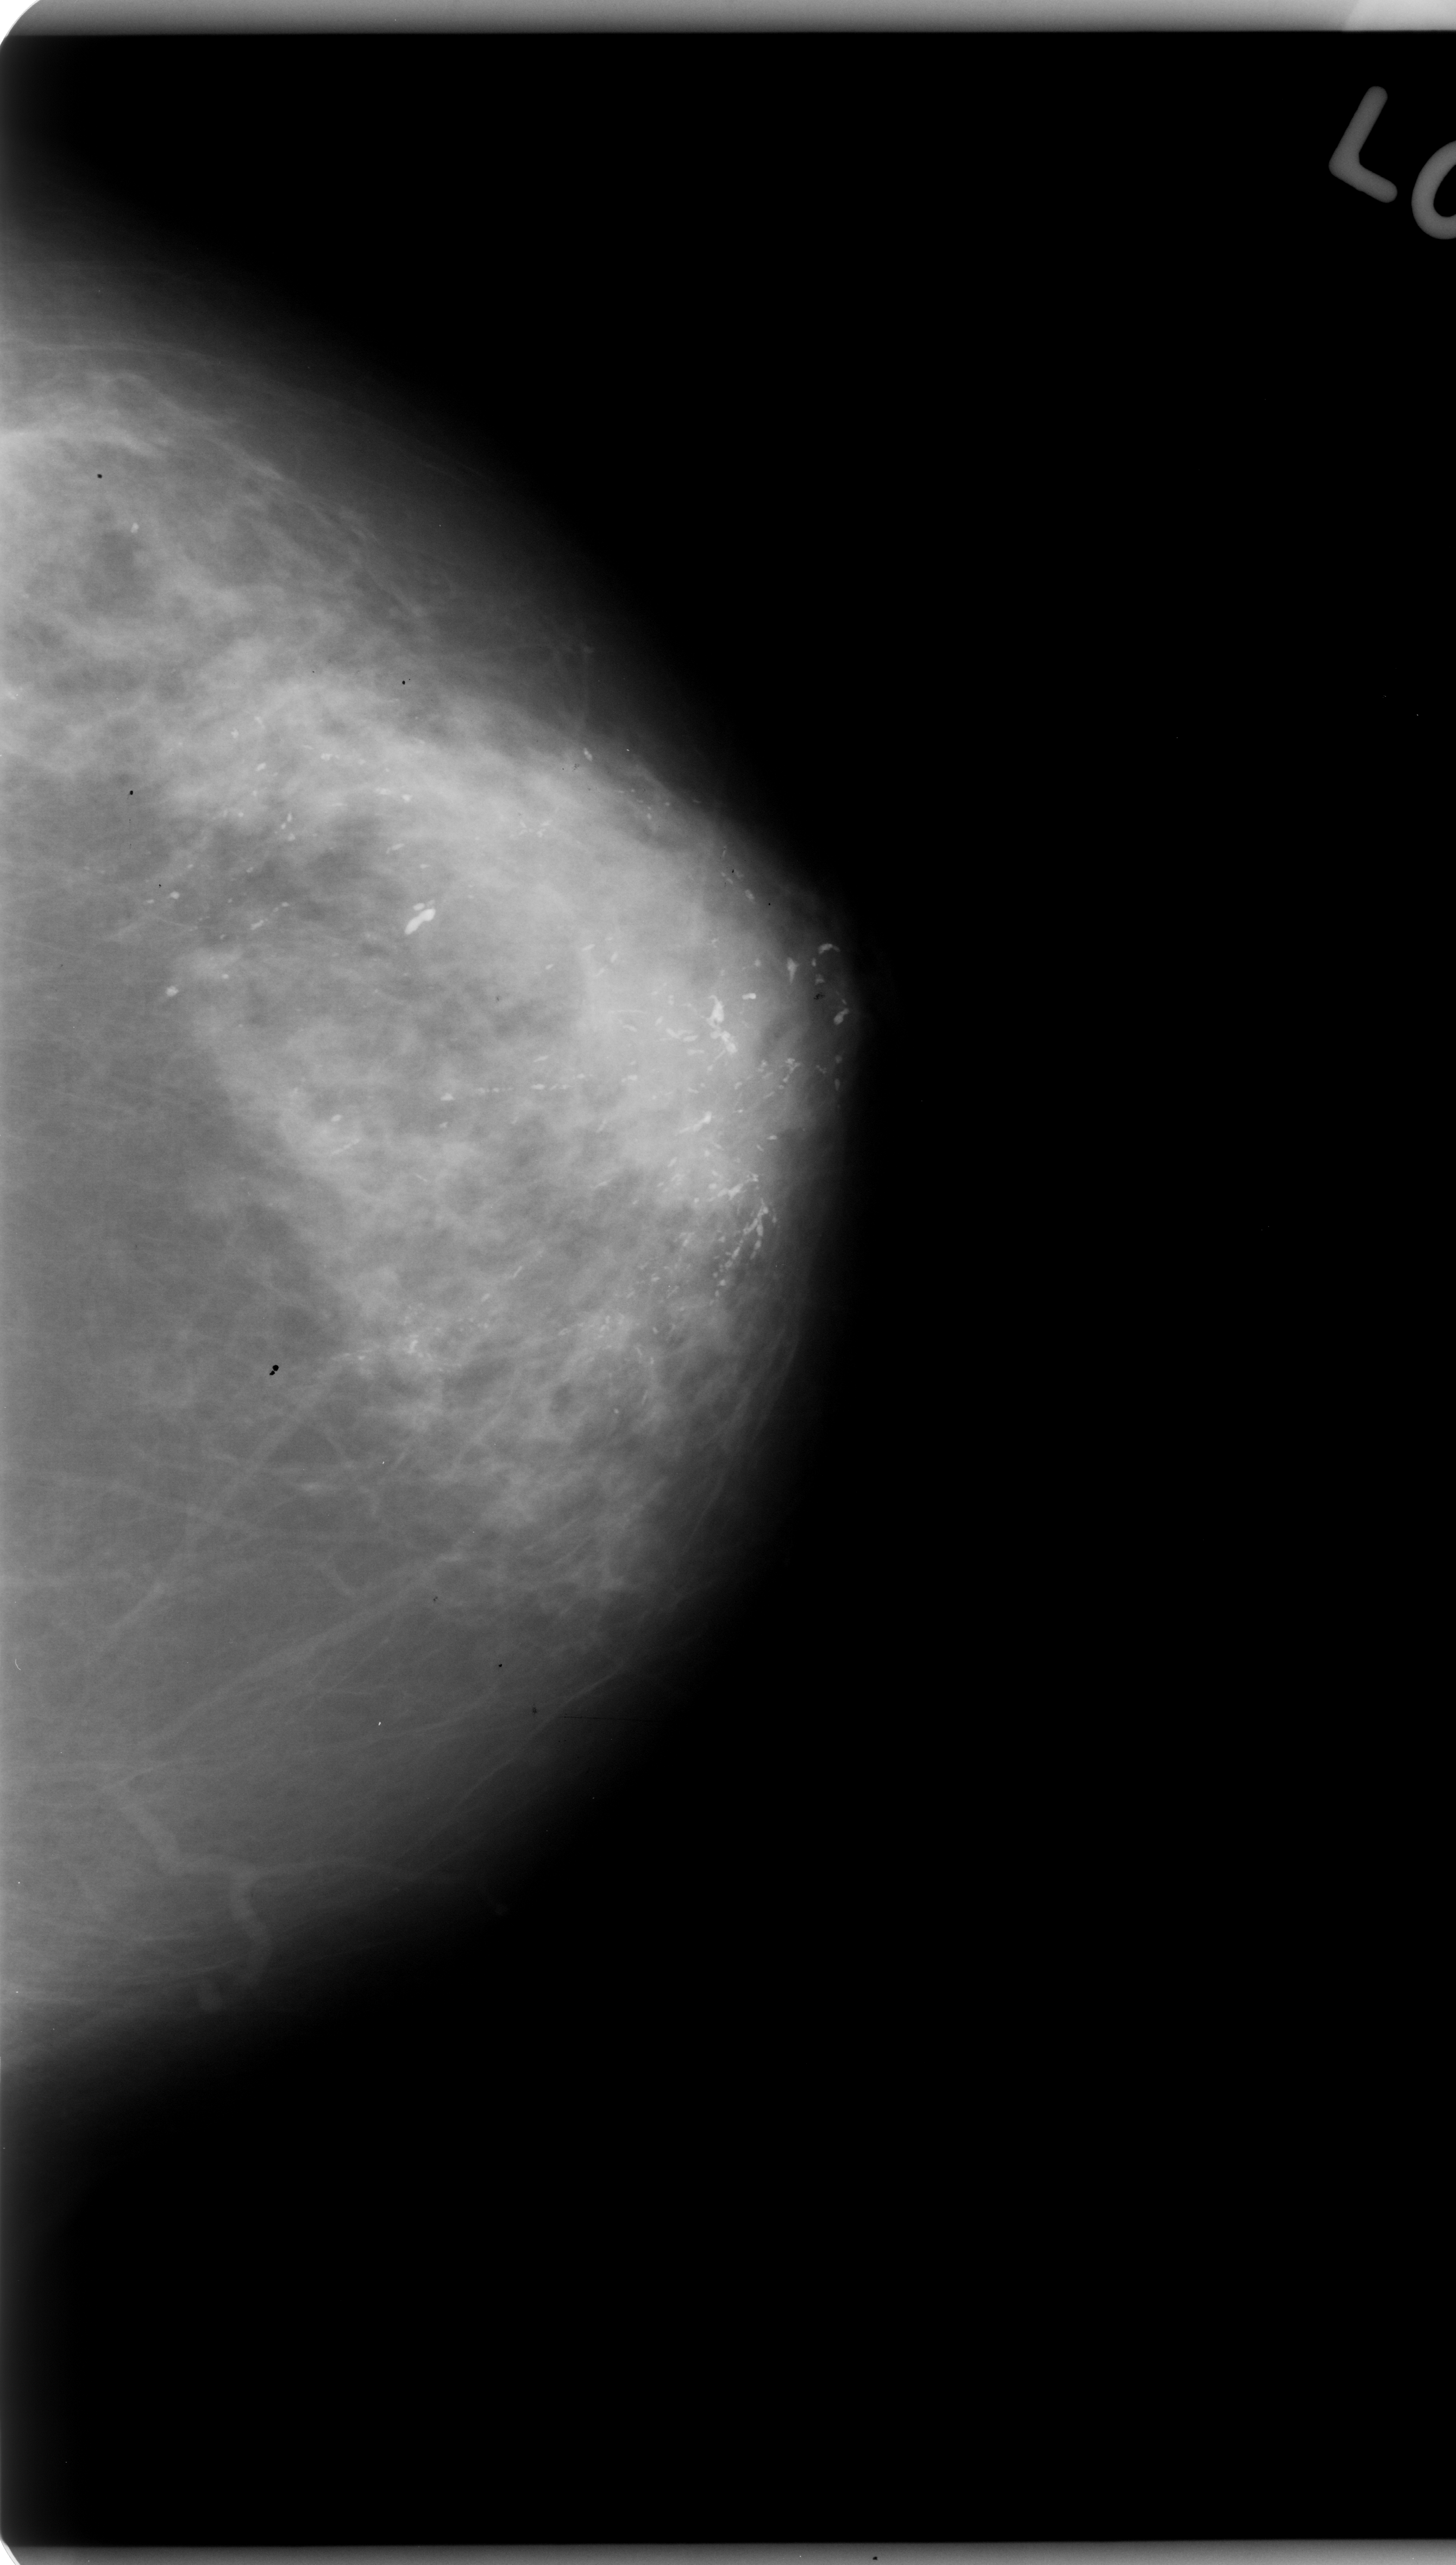
Mammogram (digitized film); left breast; craniocaudal (CC) view; BI-RADS breast density category 3 (scale 1–4).
- Abnormality record for this image: calcifications, morphology fine linear branching, distribution regional; BI-RADS assessment category 5; pathology result (as recorded, not read from the image): malignant.